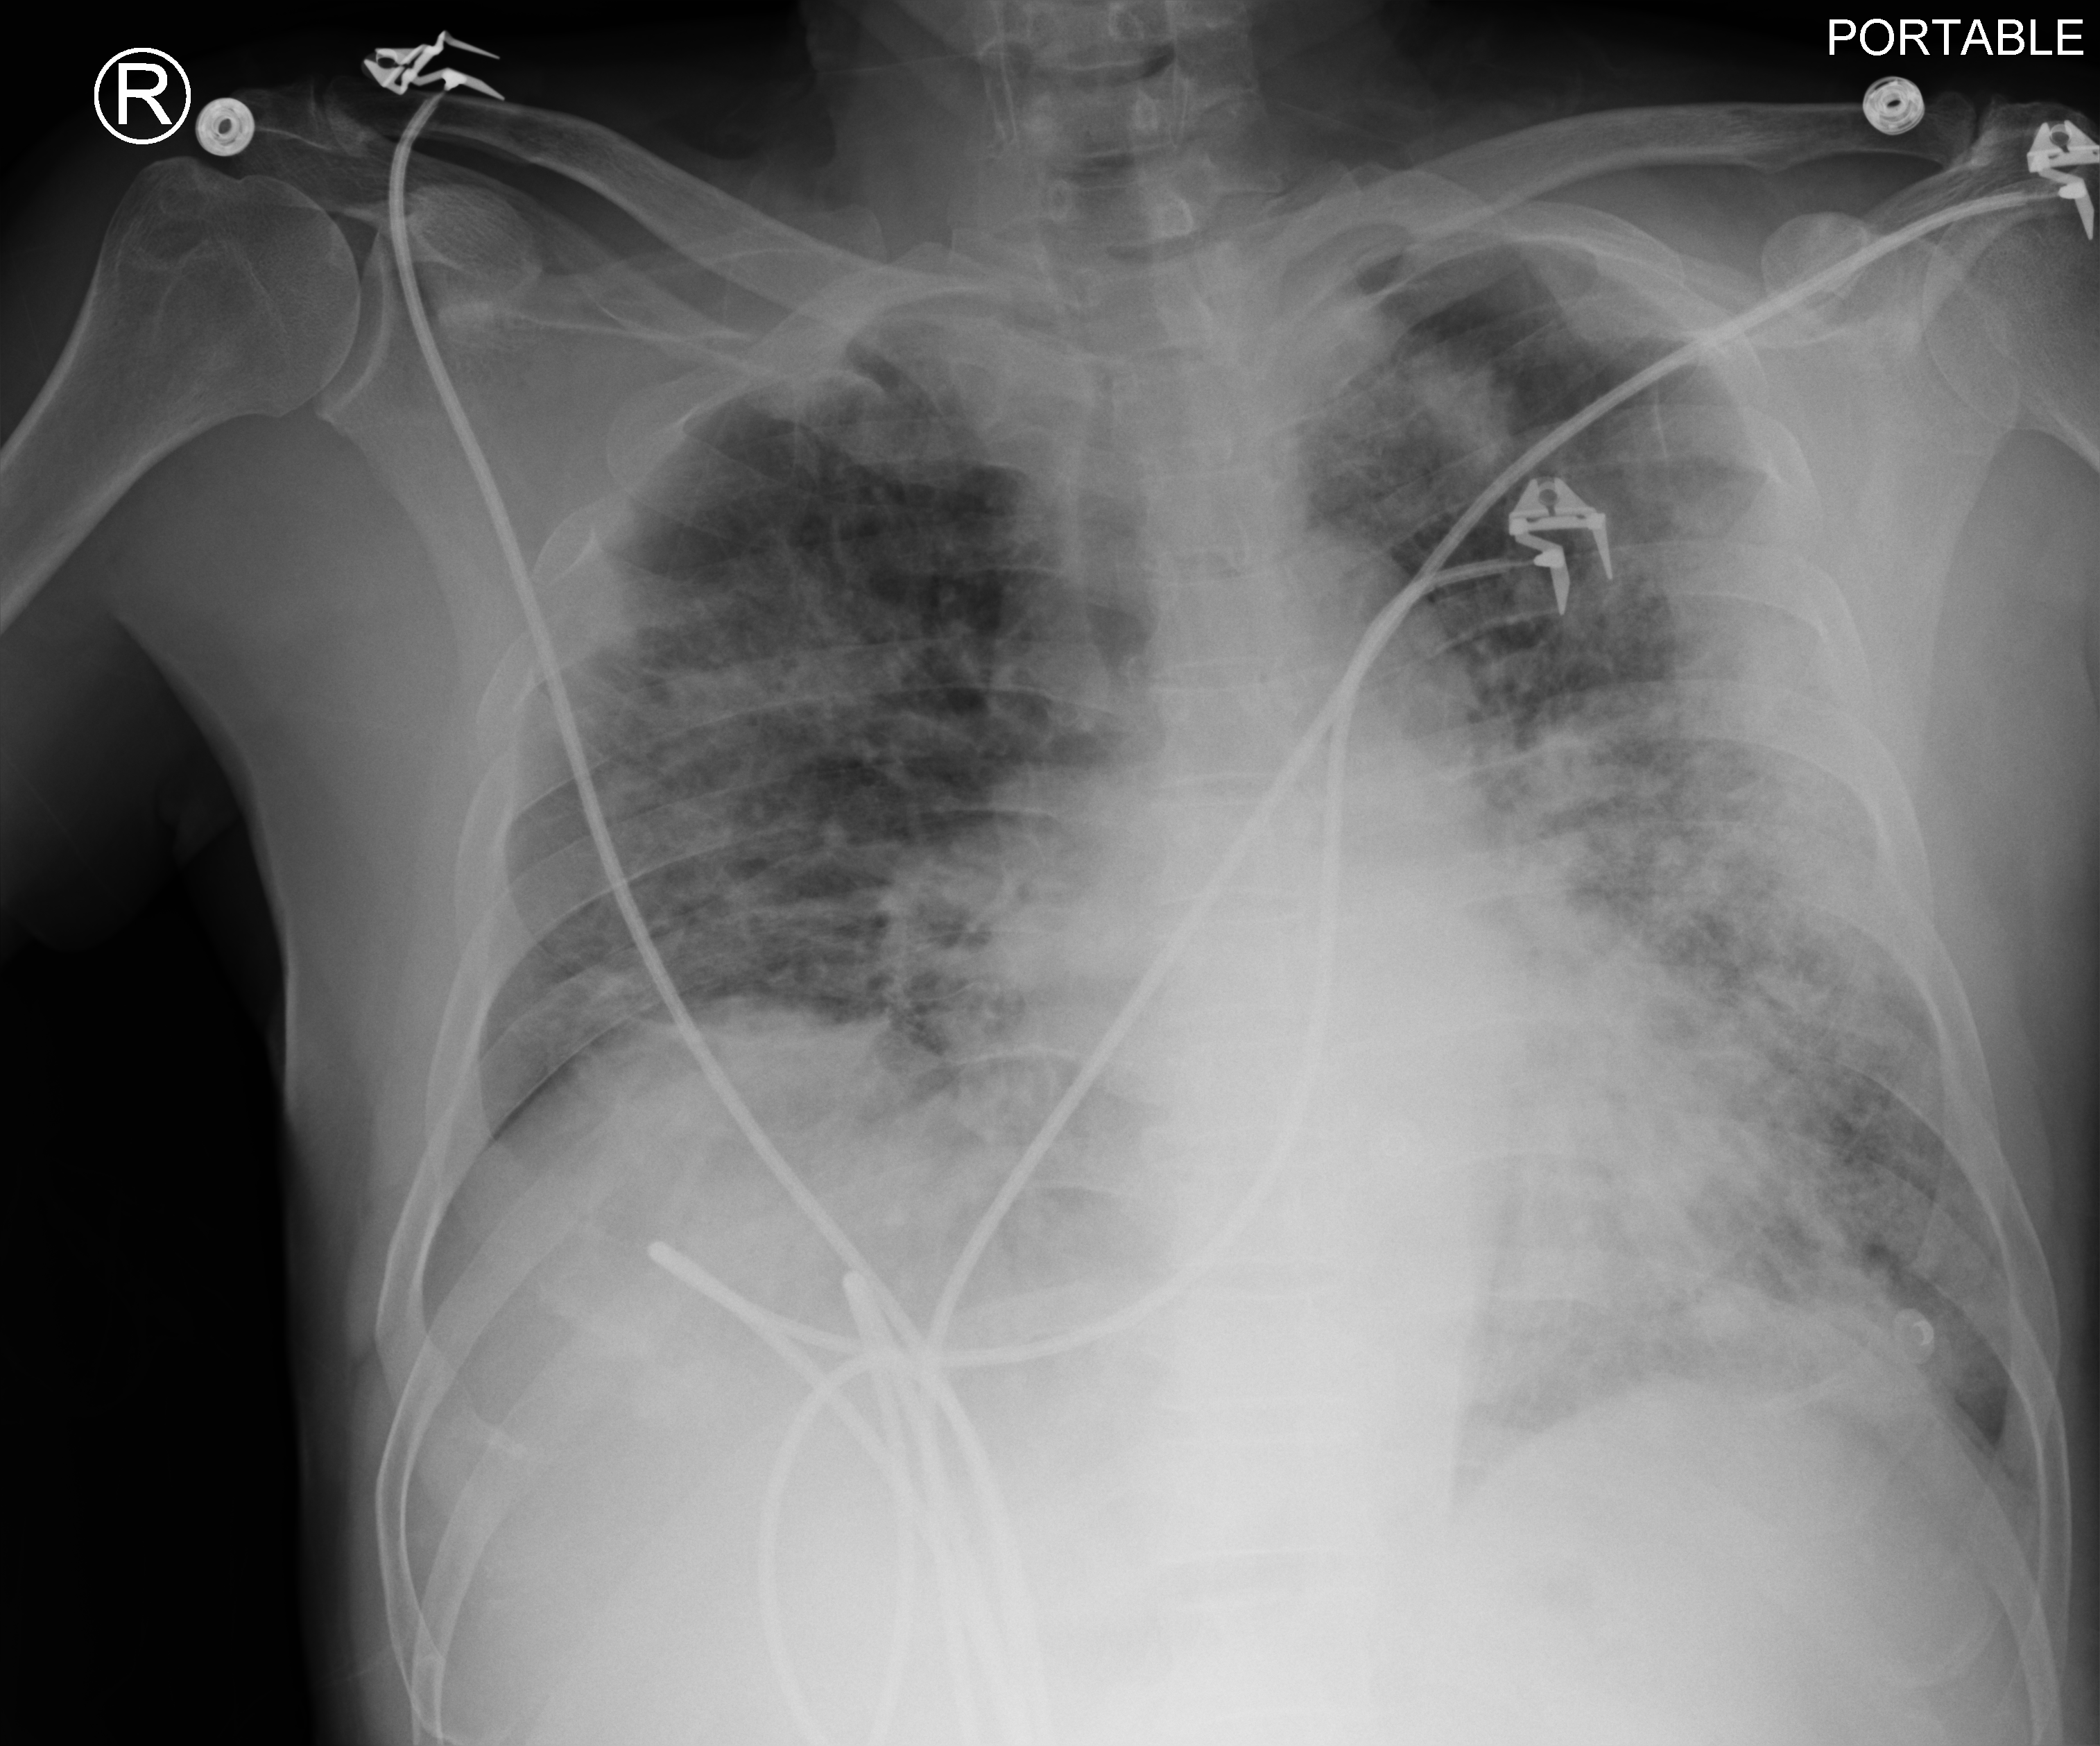
Chest X-ray (portable), anteroposterior (AP) projection. Male patient hospitalised with COVID-19, age 60–74 years.
Admission-level facts for this patient (not findings on this image; timing relative to this image not recorded):
- COPD (admission record): no
- mechanically ventilated during this hospital stay: no